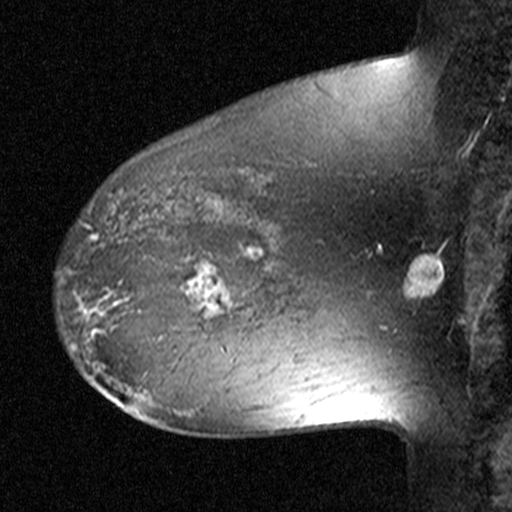
Breast MRI (dynamic contrast-enhanced), one sagittal slice; slice 31 of 44 in the series (ordered by position); dynamic contrast-enhanced study with each time point stored as its own series, time point 2 of 3 at this slice position (early post-contrast, ordered by acquisition time); 1.5 T; TE 4.5 ms, TR 11 ms; 3 mm slice thickness; 512 × 512 image matrix. Female patient, age 38 years. Case-level facts recorded for this patient, not image findings: setting: breast cancer imaged before/during neoadjuvant chemotherapy; receptor status: HR-positive, HER2-negative.
Annotated regions visible in this slice (semi-automatic segmentation, software-assisted and operator-edited):
- analysis volume of interest (the breast-tissue region the enhancement analysis was run in; not a lesion): bounding box <152,236,253,335> (left, top, right, bottom; pixels)
- tumour enhancement mask (voxels above the 90 % enhancement threshold inside the analysis volume of interest): <186,248,253,316>